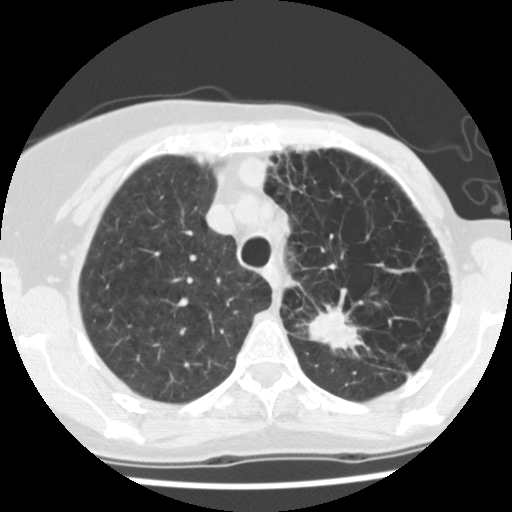
Axial slice from a low-dose chest CT screening exam. Baseline annual screen. Lung window (W 1500 / L -600 HU). 2.5 mm slice thickness. Standard (soft-tissue) reconstruction kernel (STANDARD). 512 × 512 image matrix, field of view 290 × 290 mm. Female participant, aged 67 years at enrolment. Current smoker at enrolment.
- Expert reader's lesion annotation, bounding box [x1, y1, x2, y2] px = [297, 290, 384, 368].
- The screening reader recorded 2 non-calcified nodules or masses ≥4 mm on this exam; which of them this box marks is not recorded.
- Lung cancer was diagnosed 109 days after this screen: adenocarcinoma, NOS, left upper lobe, poorly differentiated (G3), stage IIB (AJCC 6th edition), 45 mm at pathology.